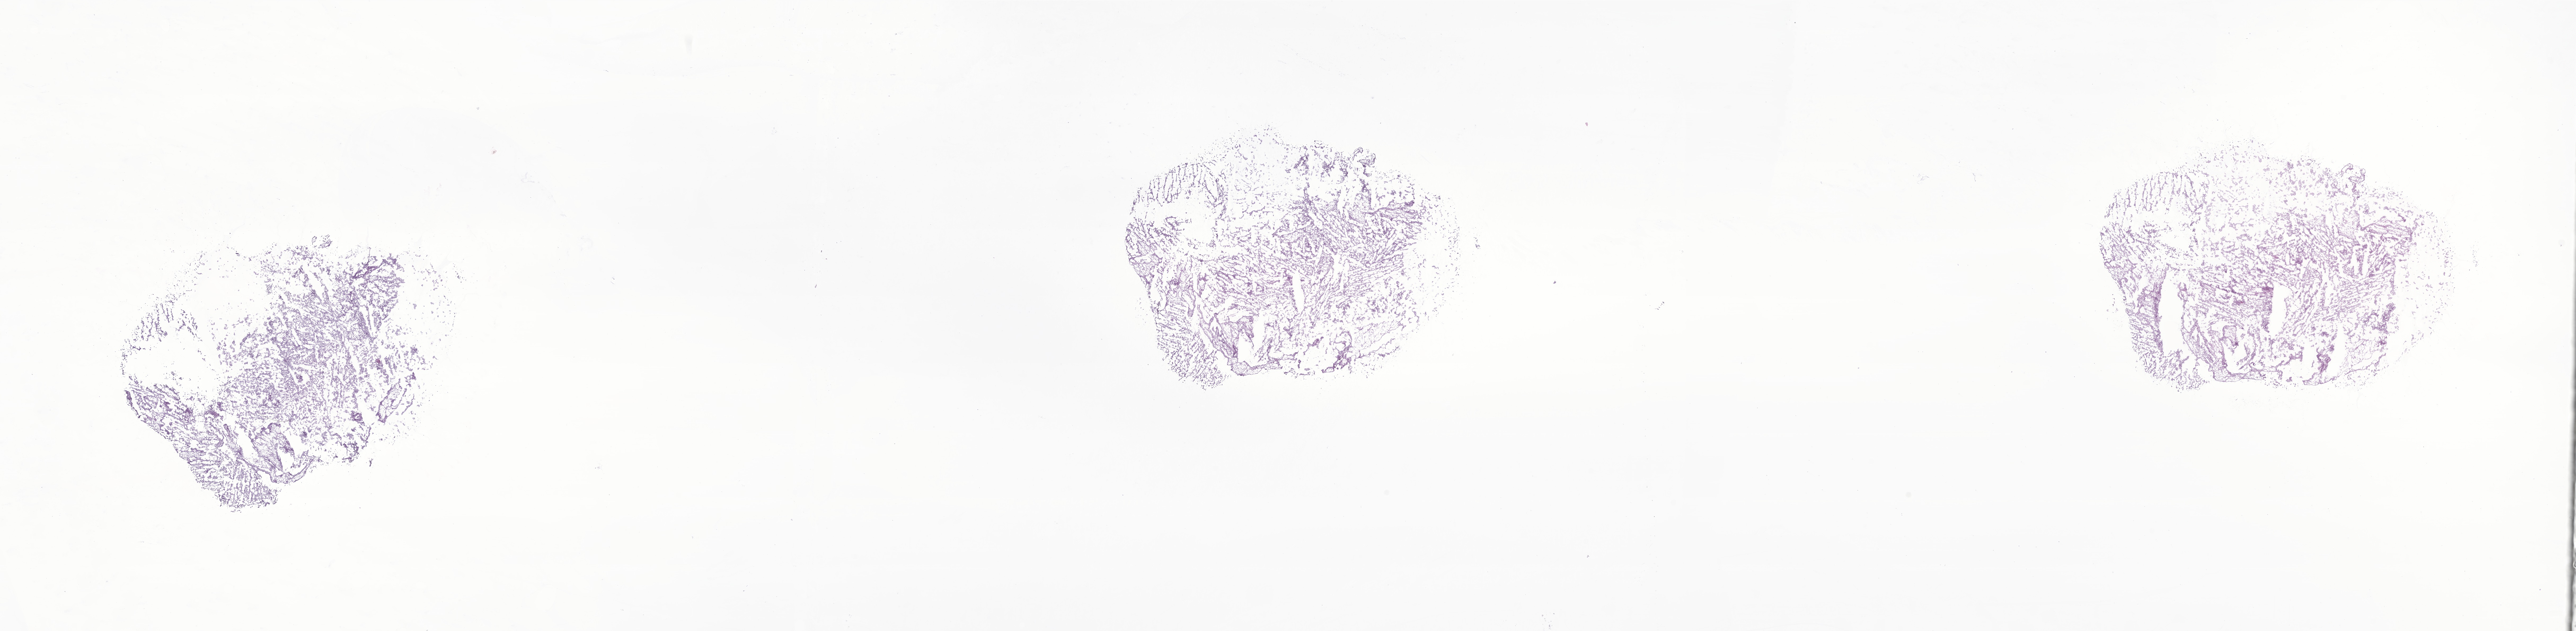
H&E whole-slide image of tumor tissue from the ovary, shown as a low-resolution overview of the whole scanned area (about 41.0 x 10.0 mm). Cryosection (OCT / tissue freezing medium). Patient female; age 150 months.
Recorded diagnosis: Granulosa cell tumor, juvenile.